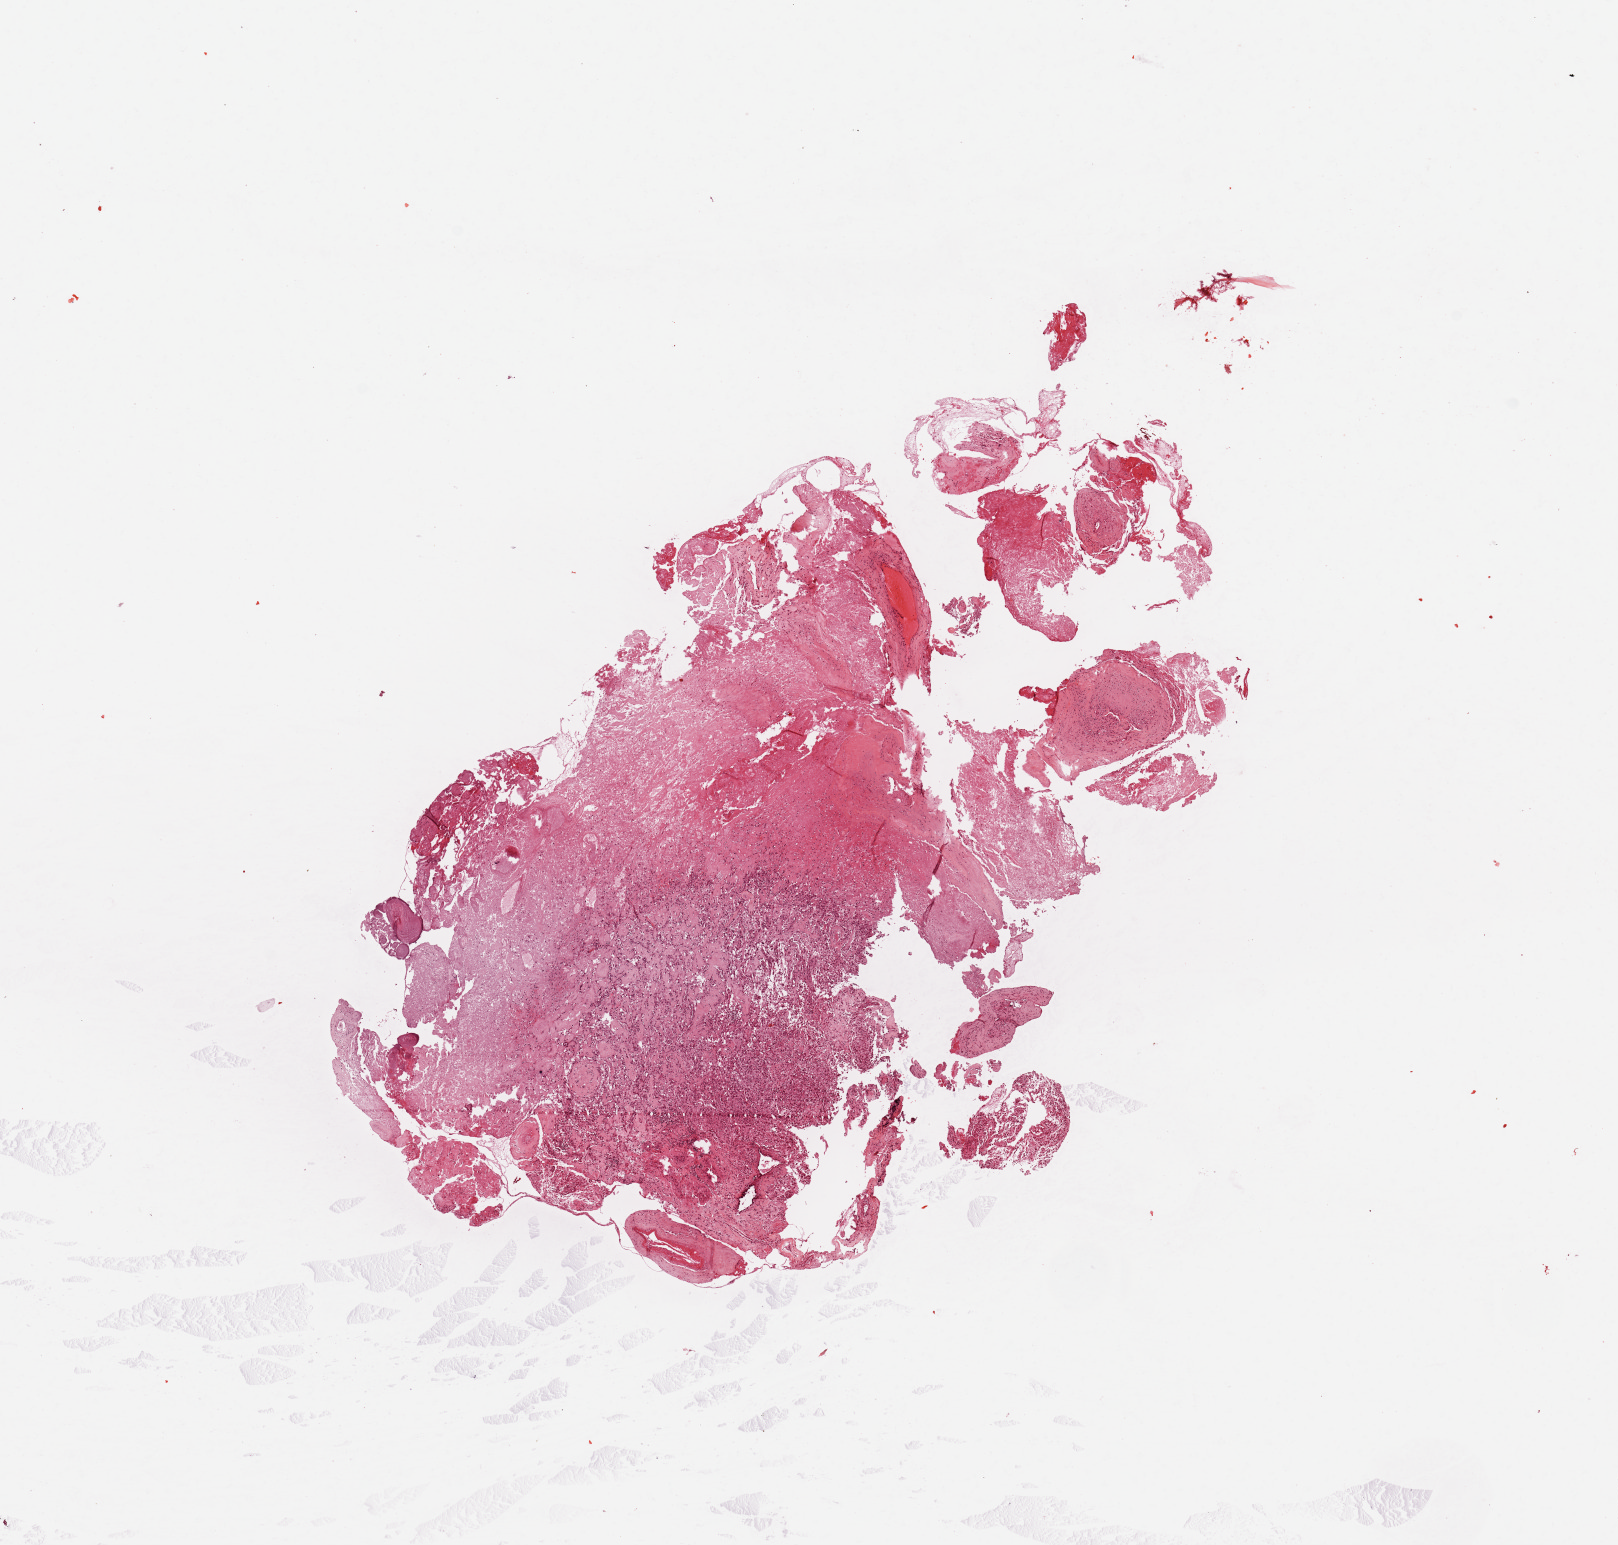
H&E whole-slide image — shown as a low-resolution overview of the whole scanned area (about 12.8 x 12.2 mm); tumour tissue sample, brain. Patient: female, age 71 years.
* primary tumour site (as recorded): left hemisphere
* diagnosis: Glioblastoma